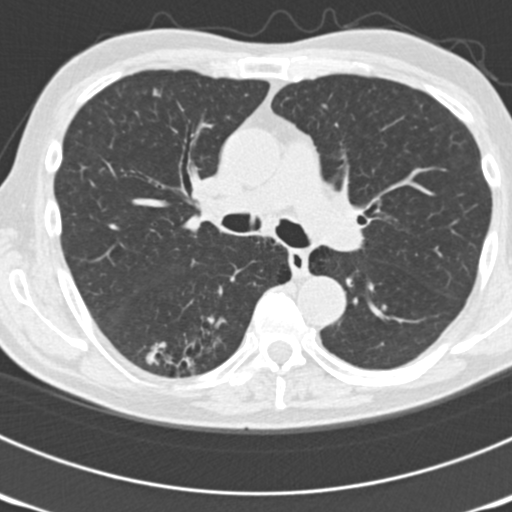
Low-dose screening chest CT, one axial slice; position 114 of 177 along the scan axis; reconstruction kernel B30f; 120 kVp; lung window (W 1500 / L -600 HU); 2 mm slice thickness; 512 × 512 image matrix, field of view 300 × 300 mm.
Outlined on this slice (manually delineated by an expert):
- lesion 1 (nodule, upper lobe of right lung): box from (x=153, y=87) to (x=161, y=98) px